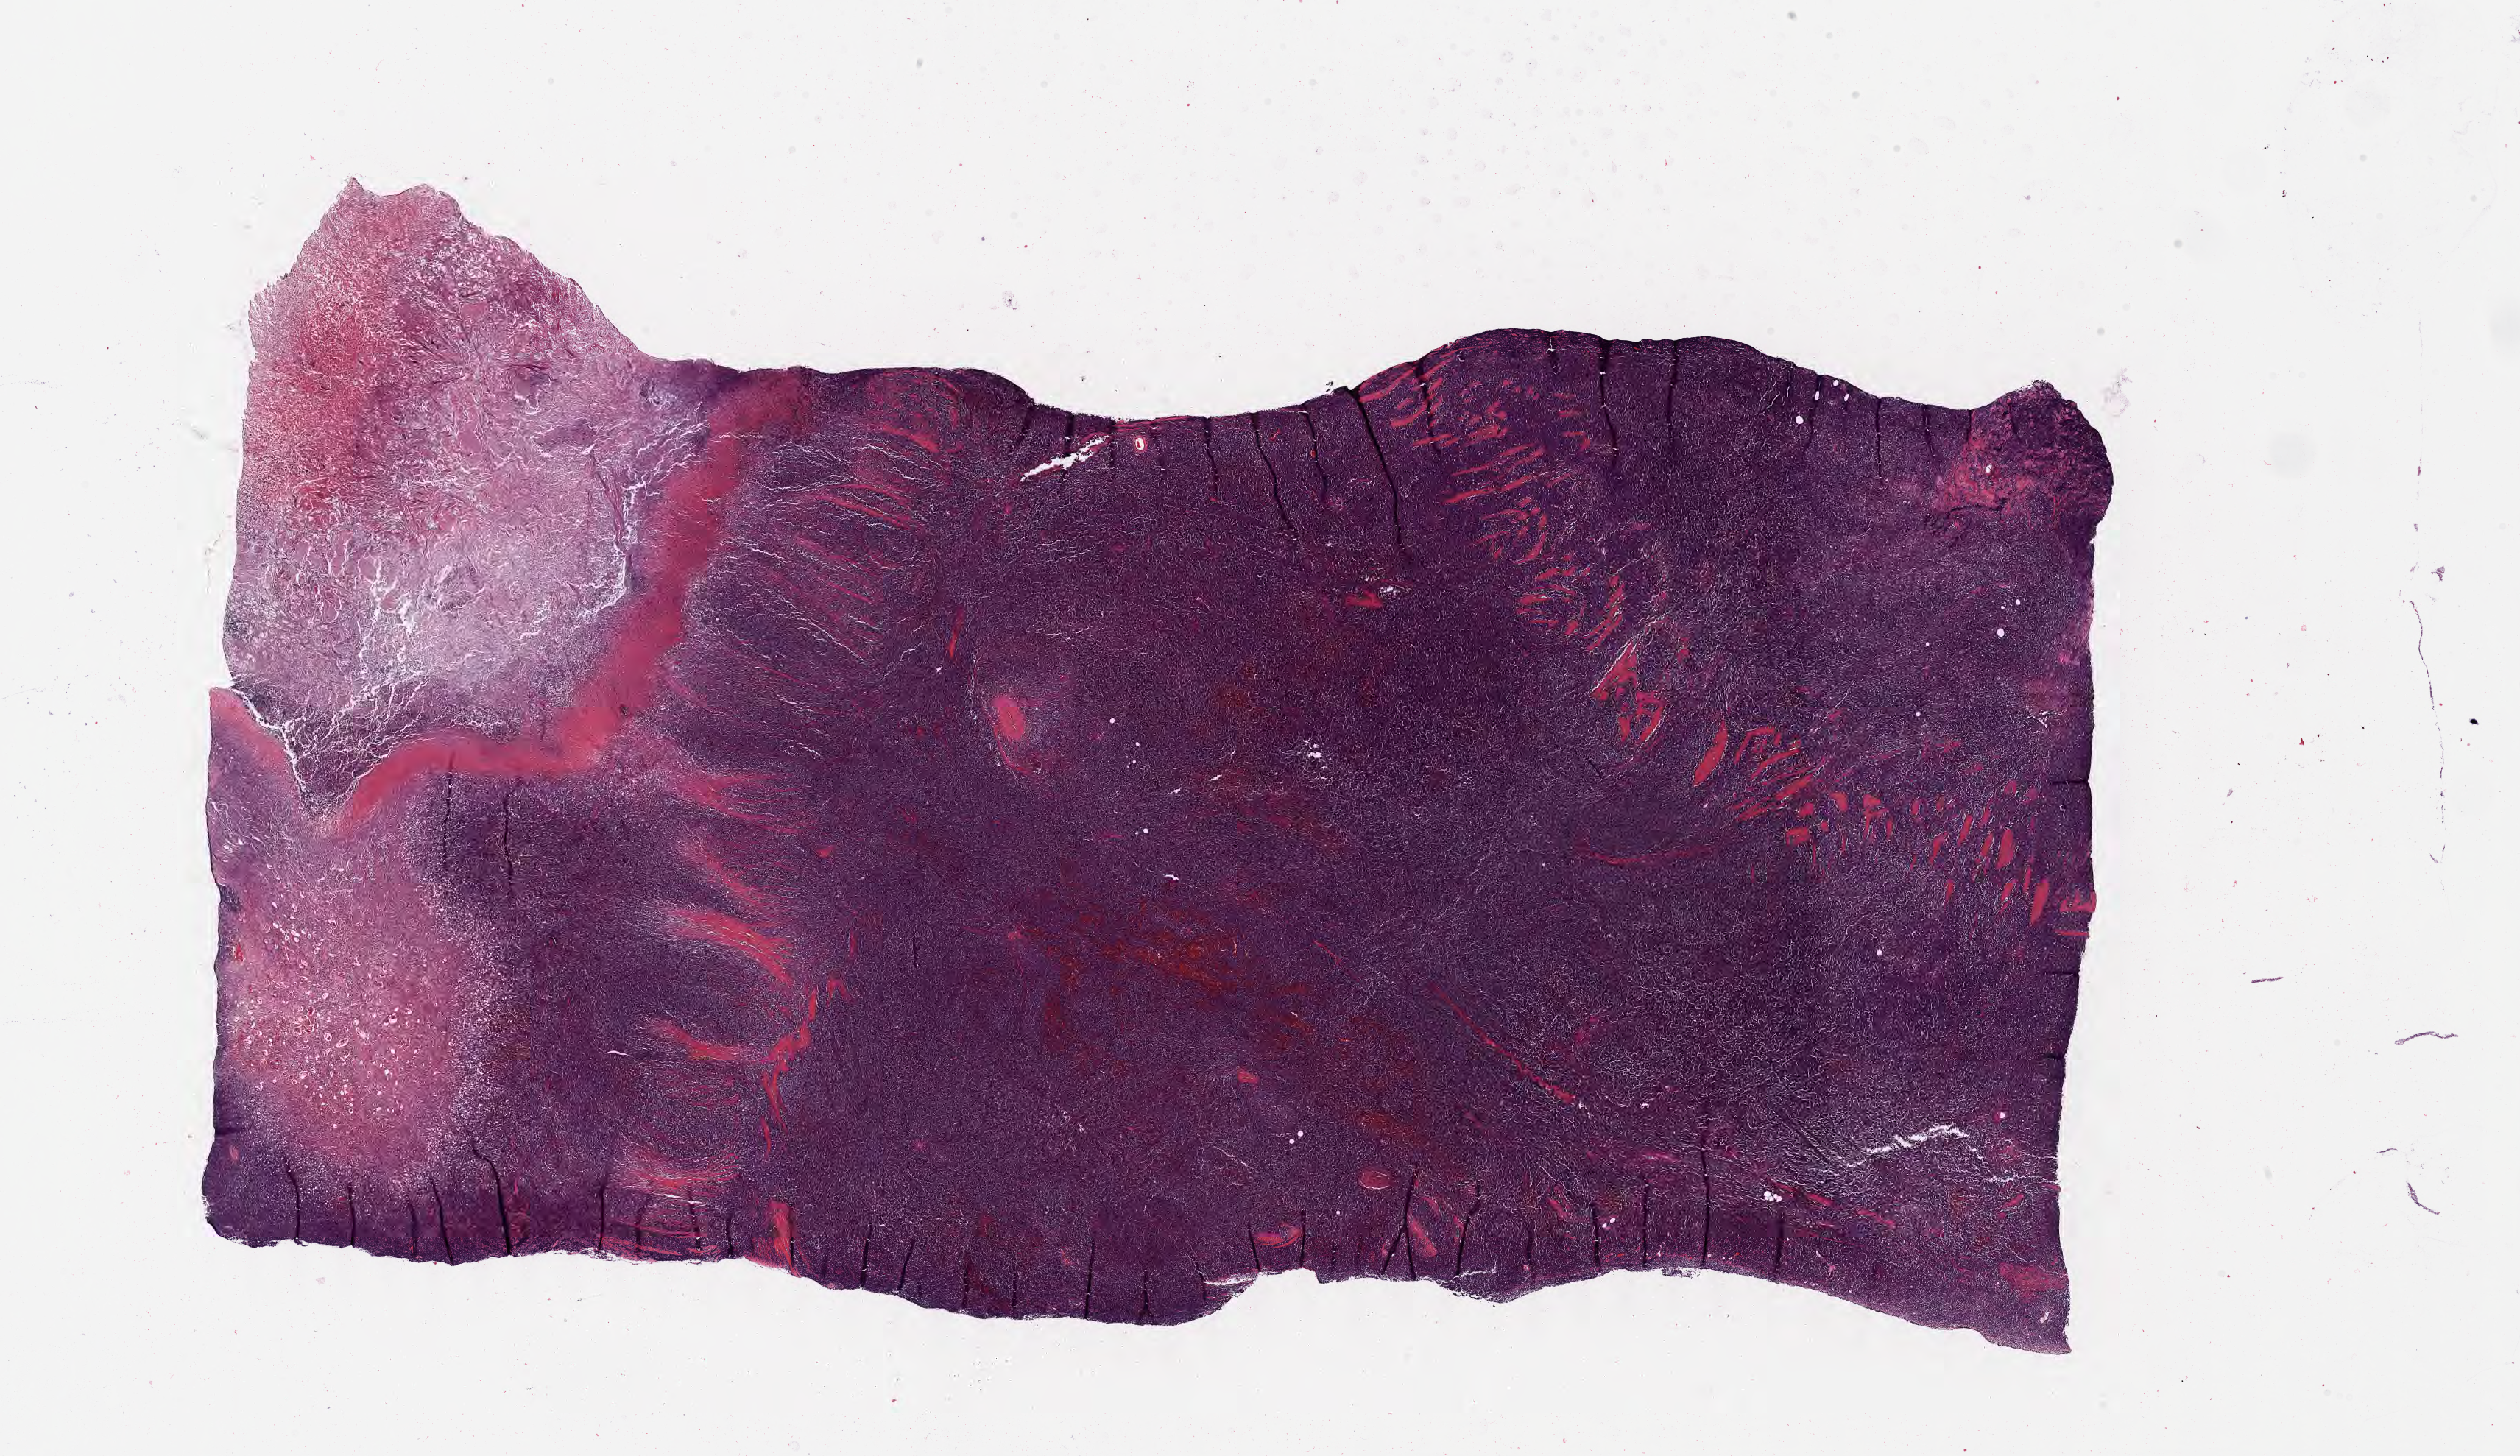
H&E whole-slide image — shown as a low-resolution overview of the whole scanned area (about 27.7 x 16.0 mm). Formalin-fixed, paraffin-embedded (FFPE) tissue. Primary tumor. Male patient, 59 years old. Pathologist review of this section (percent, as recorded): tumor cells 70%, tumor nuclei 90%, stromal cells 10%, necrosis 20%, normal cells 0%. Infiltration values recorded for this section: lymphocyte infiltration 60%, monocyte infiltration 30%, neutrophil infiltration 5%.
• histologic diagnosis: Burkitt lymphoma, NOS
• Ann Arbor stage (patient): Stage I